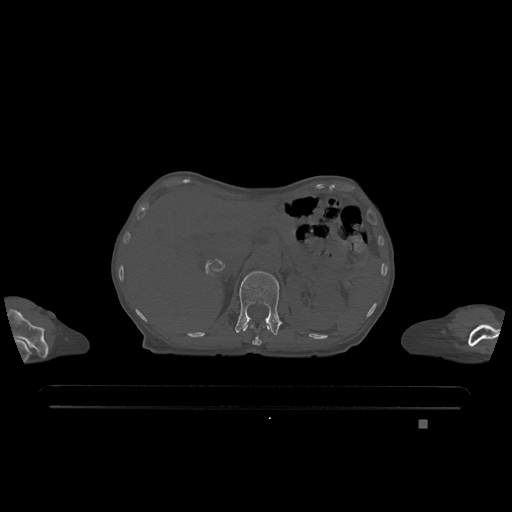
CT including the spine, one axial slice. Slice 489 of 1317 in the series (ordered by position). Bone window (W 1800 / L 400 HU). 0.5 mm slice thickness. 512 × 512 image matrix, field of view 500 × 500 mm. Female patient, age 74 years. From the clinical record (not read from this slice): primary cancer: lung; vertebrae with lytic lesions (as recorded): T1, T4, T5, T6, L4, L5.
Annotated regions visible in this slice (semi-automatic segmentation, software-assisted and operator-edited):
- L1 vertebra: bounding box <235,271,281,335> (left, top, right, bottom; pixels)
- T12 vertebra: <243,325,269,345>